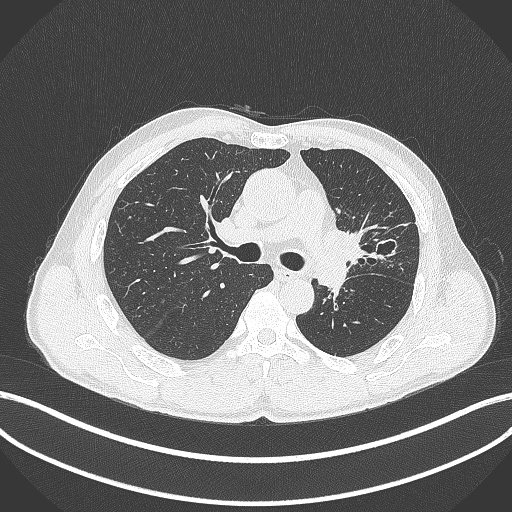
Chest CT, one axial slice; slice 262 of 429 in the series (ordered by position); 120 kVp; lung window (W 1500 / L -600 HU); 1 mm slice thickness; 512 × 512 image matrix, field of view 400 × 400 mm. Patient: male, 57 years. From the clinical record (not read from this slice): clinical TNM (as recorded): T2b N0 M0.
Annotated regions visible in this slice (bounding box drawn by a radiologist):
- lung tumour (recorded histology: squamous cell carcinoma): bounding box [x1, y1, x2, y2] px = [320, 223, 373, 268]